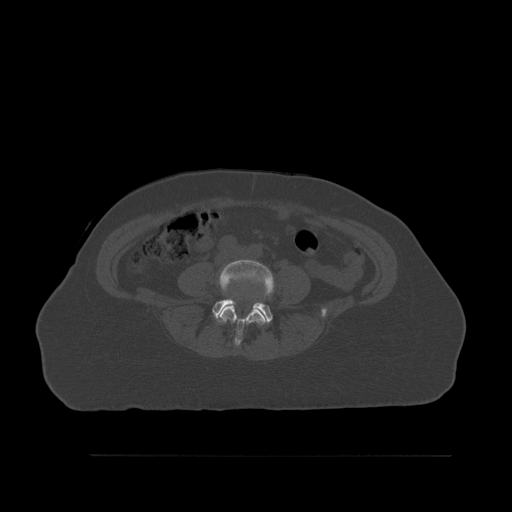
CT including the spine, one axial slice; position 199 of 527 along the scan axis; bone window (W 1800 / L 400 HU); 512 × 512 image matrix, field of view 470 × 470 mm. Female patient, age 73 years. Case-level facts recorded for this patient, not image findings: primary cancer: breast.
Annotated regions visible in this slice (semi-automatically segmented with operator editing):
- L4 vertebra: bounding box <218,259,275,347> (left, top, right, bottom; pixels)
- L5 vertebra: <212,298,273,325>